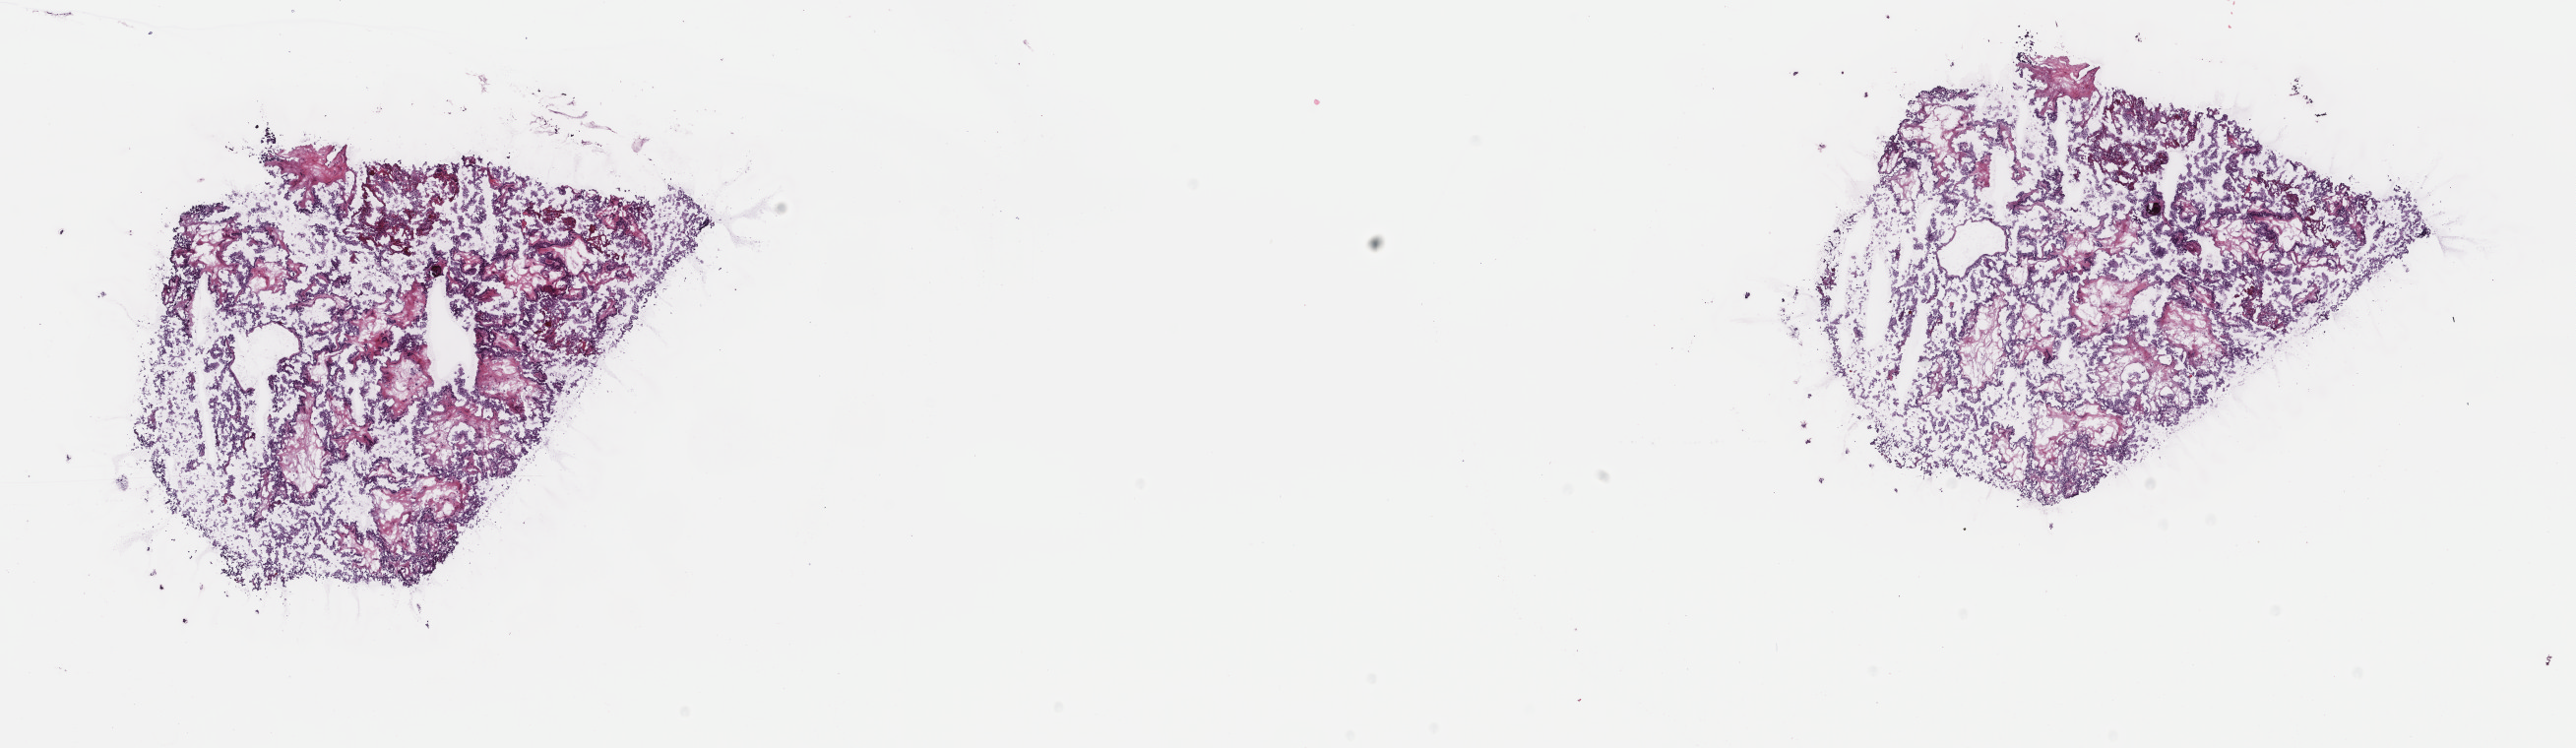
Digitized H&E-stained tissue section (whole slide) — whole scanned area (about 20.8 x 6.0 mm, slide scanned at 40x) shown as a low-resolution overview, frozen section from the top of the tissue portion, primary tumour sample from the thyroid. Male, age 63 years at initial diagnosis. Pathologist review of this section (percent, as recorded): tumour cells 80%, tumour nuclei 100%, normal cells 0%, stromal cells 20%, necrosis 0%. Infiltration values recorded for this section: lymphocyte infiltration 0%, monocyte infiltration 0%, neutrophil infiltration 0%.
AJCC pathologic stage: II (5th edition). Pathologic diagnosis: Papillary adenocarcinoma, NOS (thyroid gland). TNM: T2 N0 M0. Laterality: left.